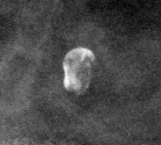
Cropped region of a digitized screen-film mammogram centred on a radiologist-marked abnormality; left breast; MLO view; BI-RADS breast density category 2 (scale 1–4).
Marked abnormality: calcifications, morphology vascular / coarse / lucent centered; BI-RADS assessment category 2; subtlety rating 5 on a 1 (subtle) to 5 (obvious) scale; benign without callback (not worked up further).